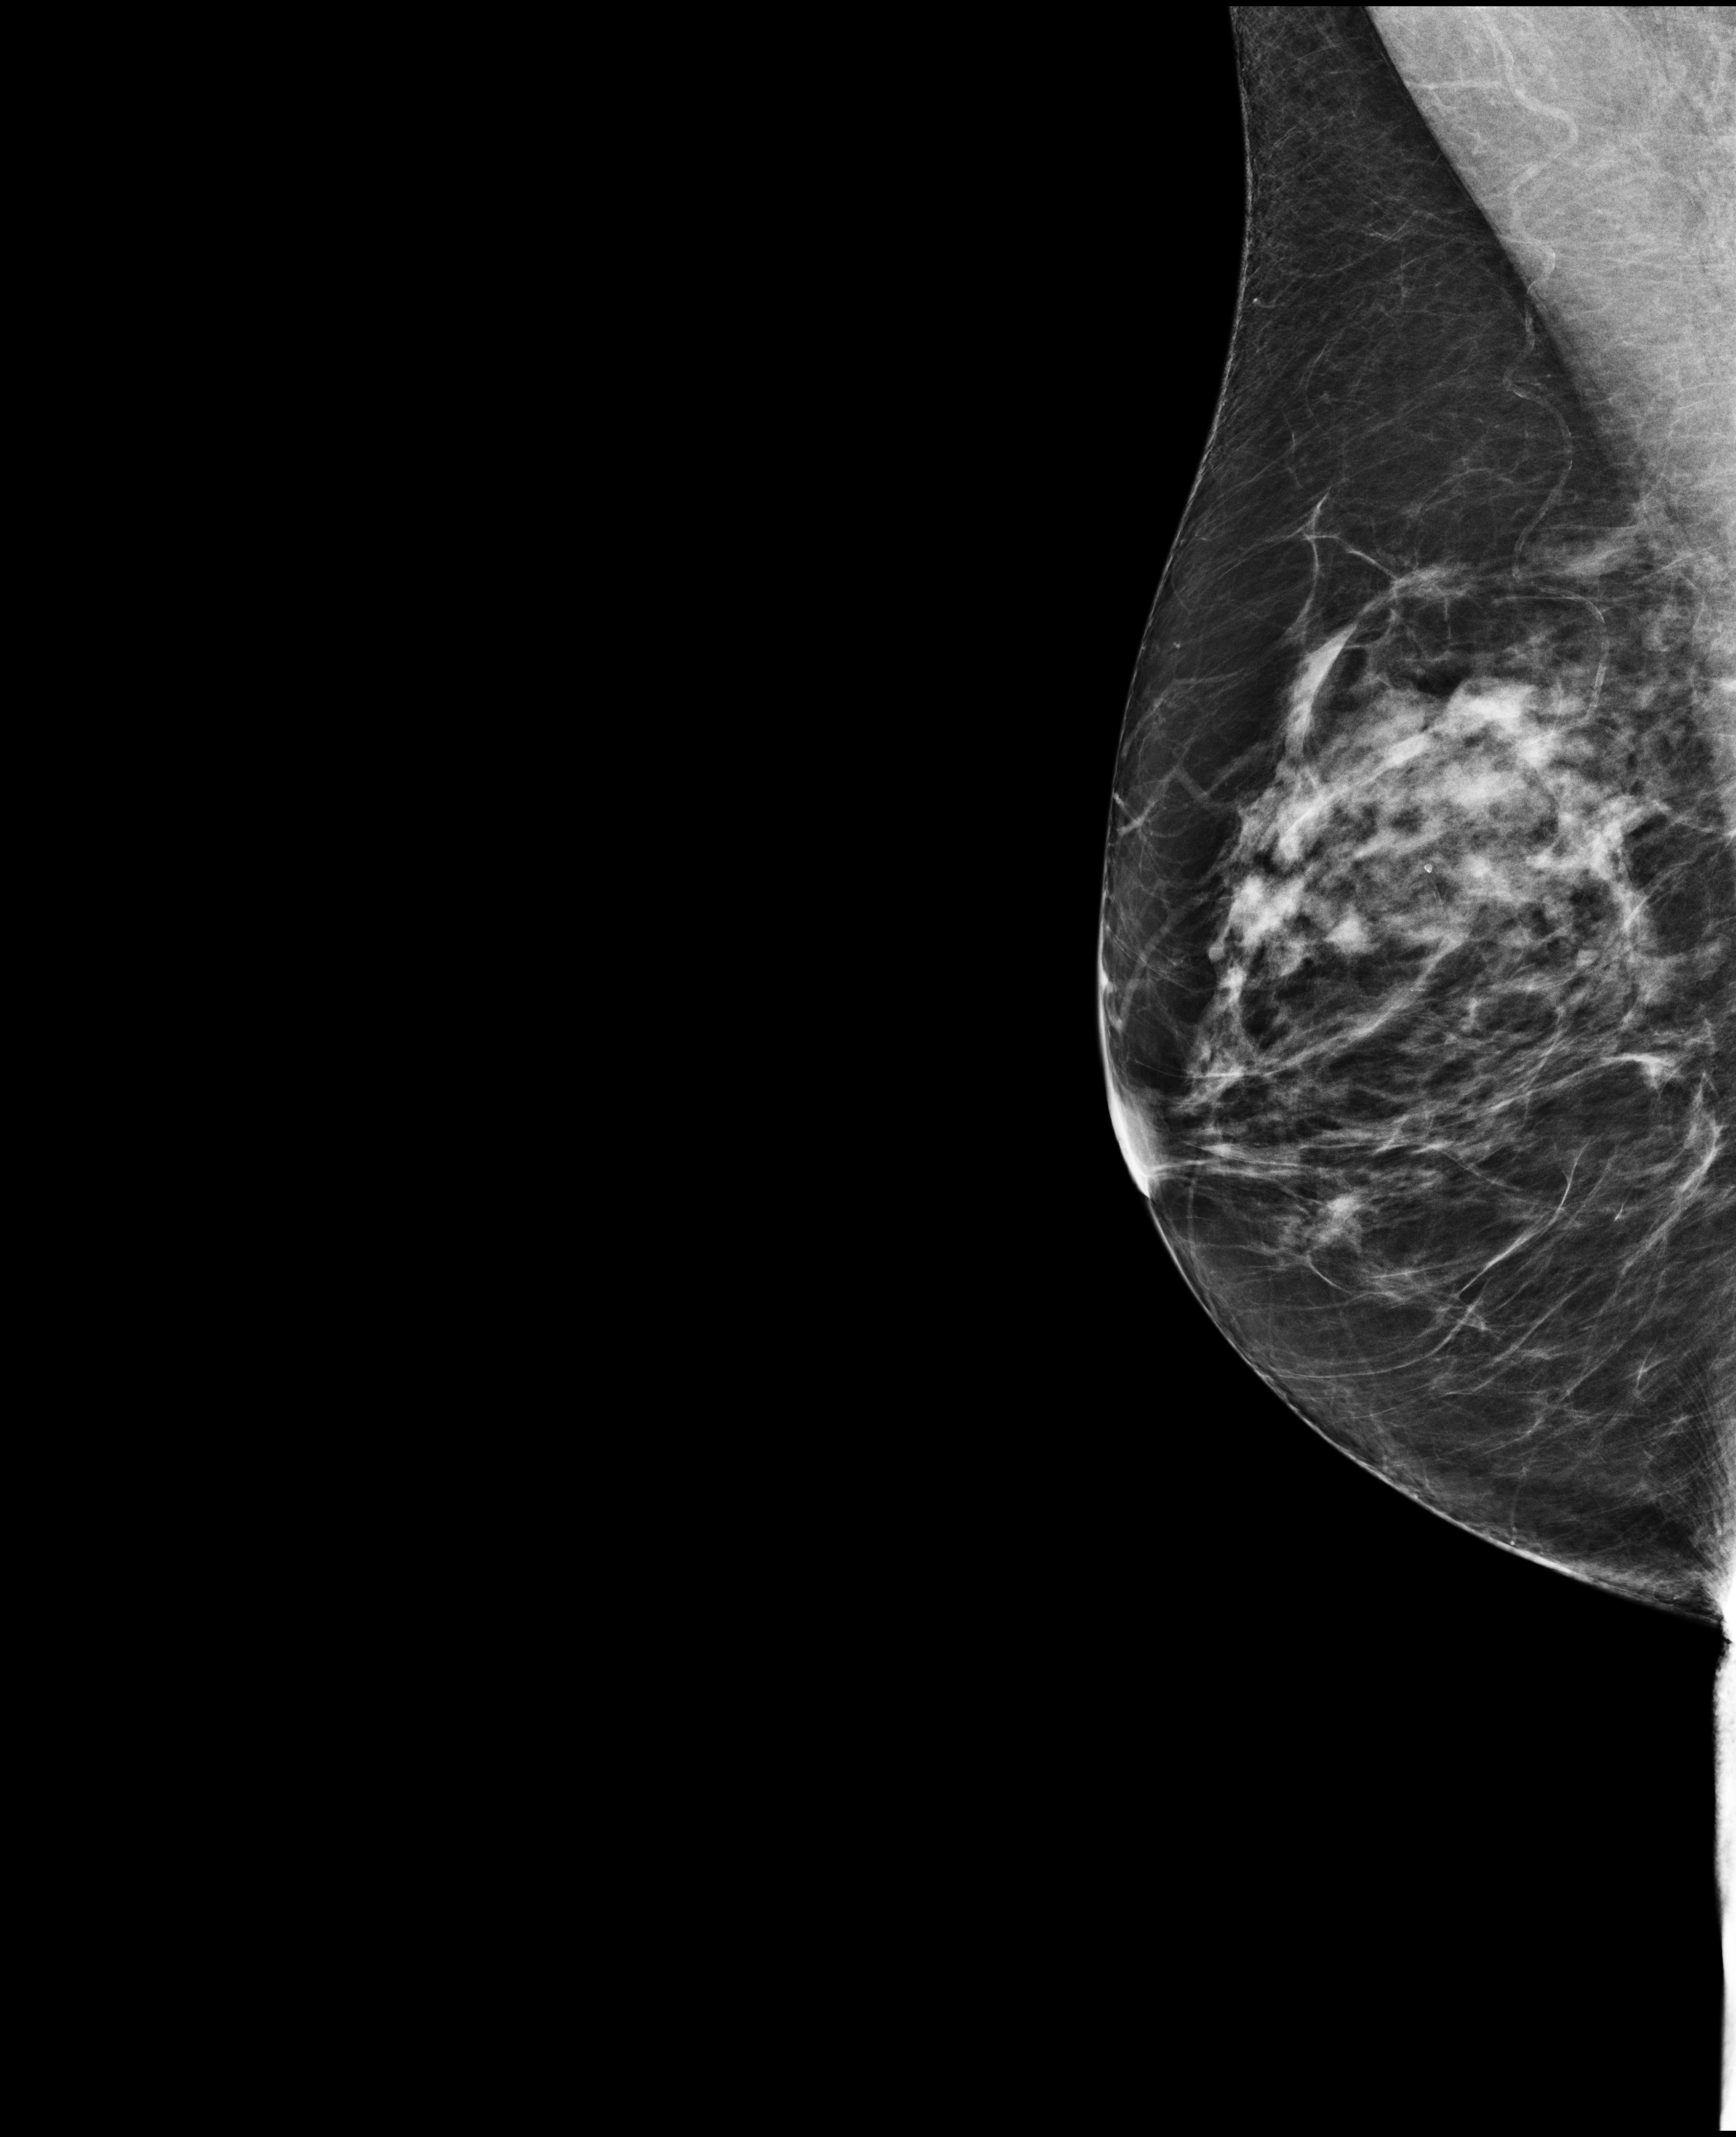
Full-field digital mammogram (FFDM), right breast, mediolateral oblique (MLO) view, annual screening mammography examination, system: Selenia Dimensions. Patient: female, 67 years.
- BI-RADS breast density category at the screening exam (both breasts, scale 1–4): 3
- final BI-RADS category for the screening round (tomosynthesis exam, both breasts): category 1
- recall: no recall after this screen